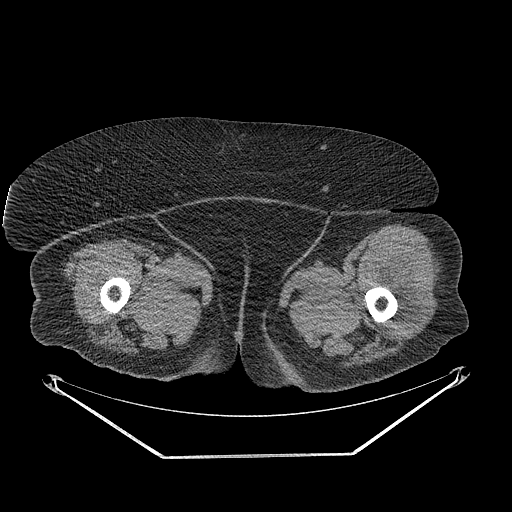
CT of an extremity soft-tissue mass (from a PET/CT study), one axial slice. Position 255 of 267 along the scan axis. Reconstruction kernel STANDARD. Soft-tissue window (W 400 / L 40 HU). 512 × 512 image matrix, field of view 500 × 500 mm. Female patient. Case-level facts recorded for this patient, not image findings: histological type: undifferentiated – high grade; grade: high; site of the primary tumour: left thigh.
Annotated regions visible in this slice (expert contour drawn on MRI and transferred to this co-registered scan by the dataset authors):
- gross tumour volume including surrounding oedema: bounding box [x1, y1, x2, y2] px = [381, 267, 421, 336]
- gross tumour volume (mass): [390, 304, 417, 328]